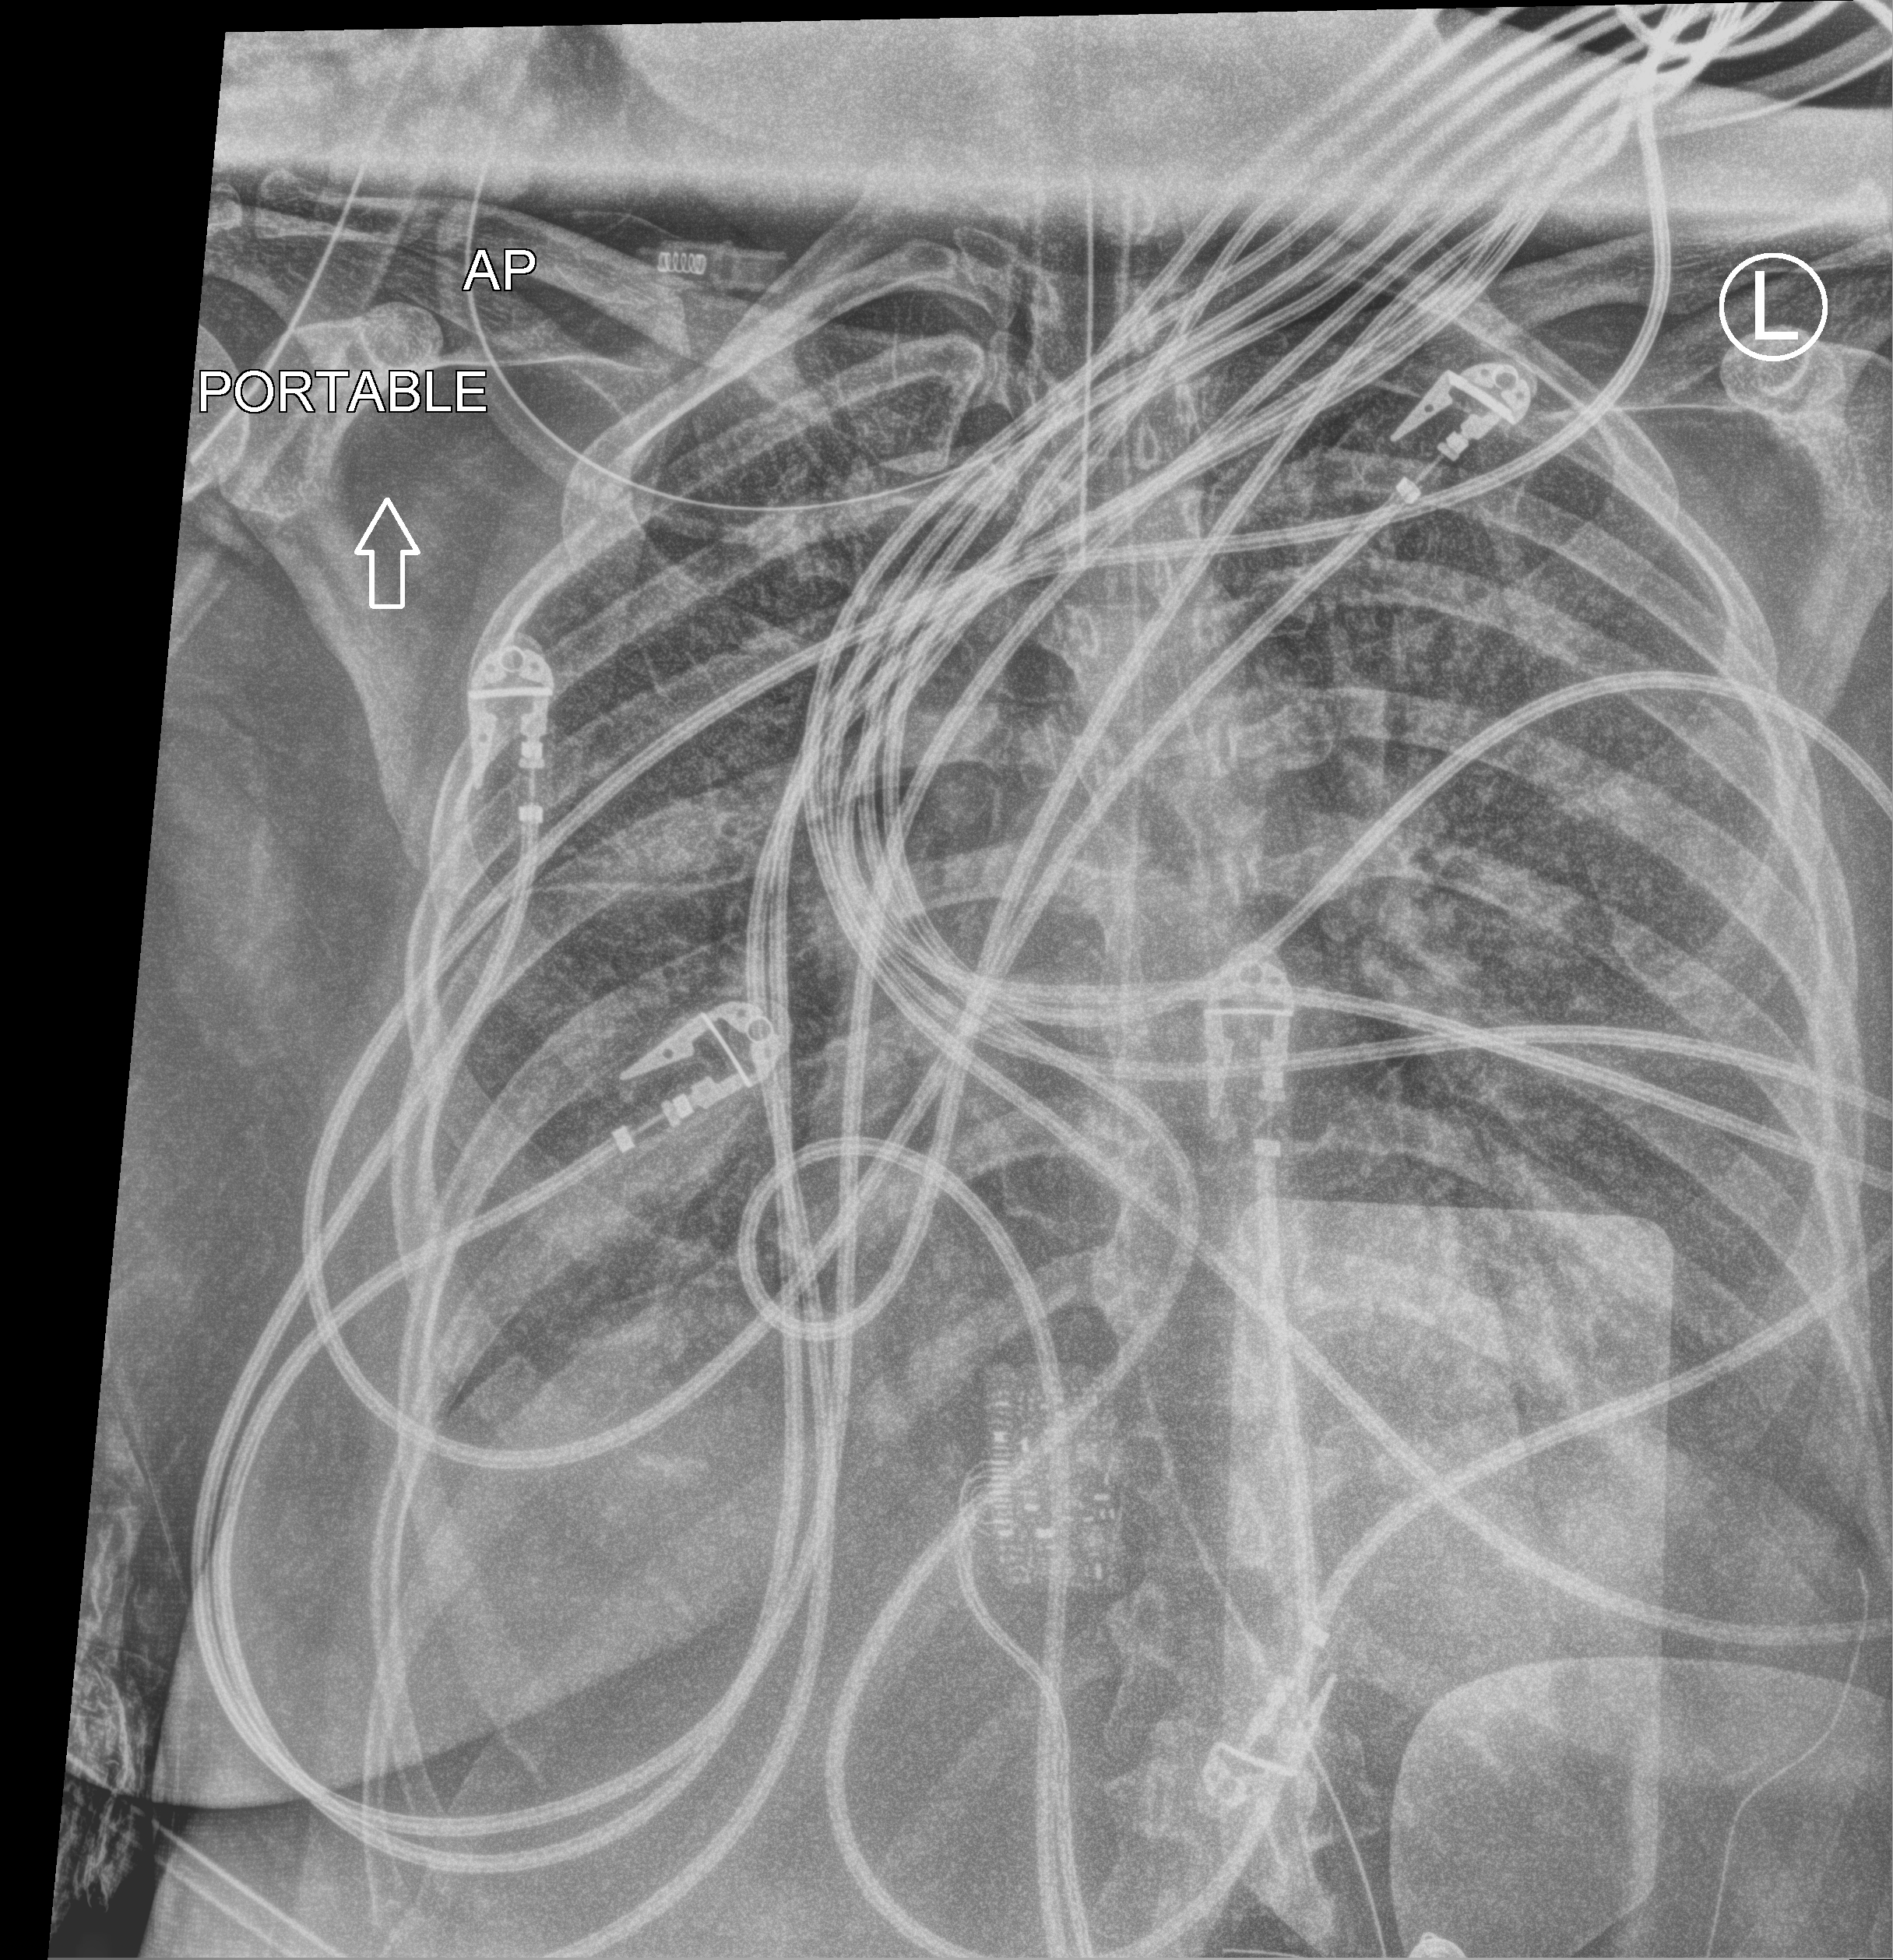
Chest X-ray (portable); anteroposterior (AP) projection. Patient hospitalised with COVID-19; male, aged 18–59 years.
Hospital-stay facts (about this admission, not read from this image; timing relative to this image not recorded):
- smoking status (admission record): never
- other chronic lung disease (admission record): no
- length of hospital stay: 38 days